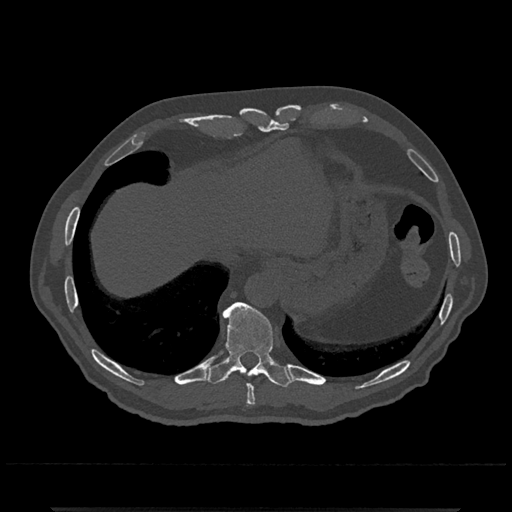
CT including the spine, one axial slice; position 568 of 797 along the scan axis; 120 kVp; bone window (W 1800 / L 400 HU); 0.5 mm slice thickness; 512 × 512 image matrix. Male patient, age 67 years. Case-level facts recorded for this patient, not image findings: primary cancer: prostate.
Annotated regions visible in this slice (semi-automatically segmented with operator editing):
- T10 vertebra: box from (x=206, y=302) to (x=292, y=388) px
- T9 vertebra: (x=246, y=384)–(x=256, y=407)